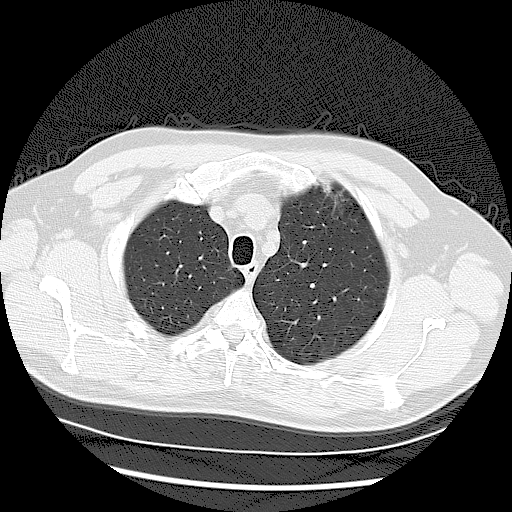
Axial slice from a low-dose chest CT screening exam, baseline screening round, lung window (W 1500 / L -600 HU), 2.5 mm slice thickness, lung (sharp) reconstruction kernel (LUNG), 120 kVp, 512 × 512 image matrix, field of view 360 × 360 mm. Male participant, aged 56 years at enrolment. Former smoker at enrolment.
Lesion marked by an expert reader, bounding box (x1, y1, x2, y2) in pixels: (315, 183, 354, 224). Screening reader's record for this exam: no non-calcified nodule ≥4 mm recorded. Lung cancer was diagnosed 834 days after this screen: adenocarcinoma, NOS, left upper lobe, moderately differentiated (G2), stage IA (AJCC 6th edition), 15 mm at pathology.